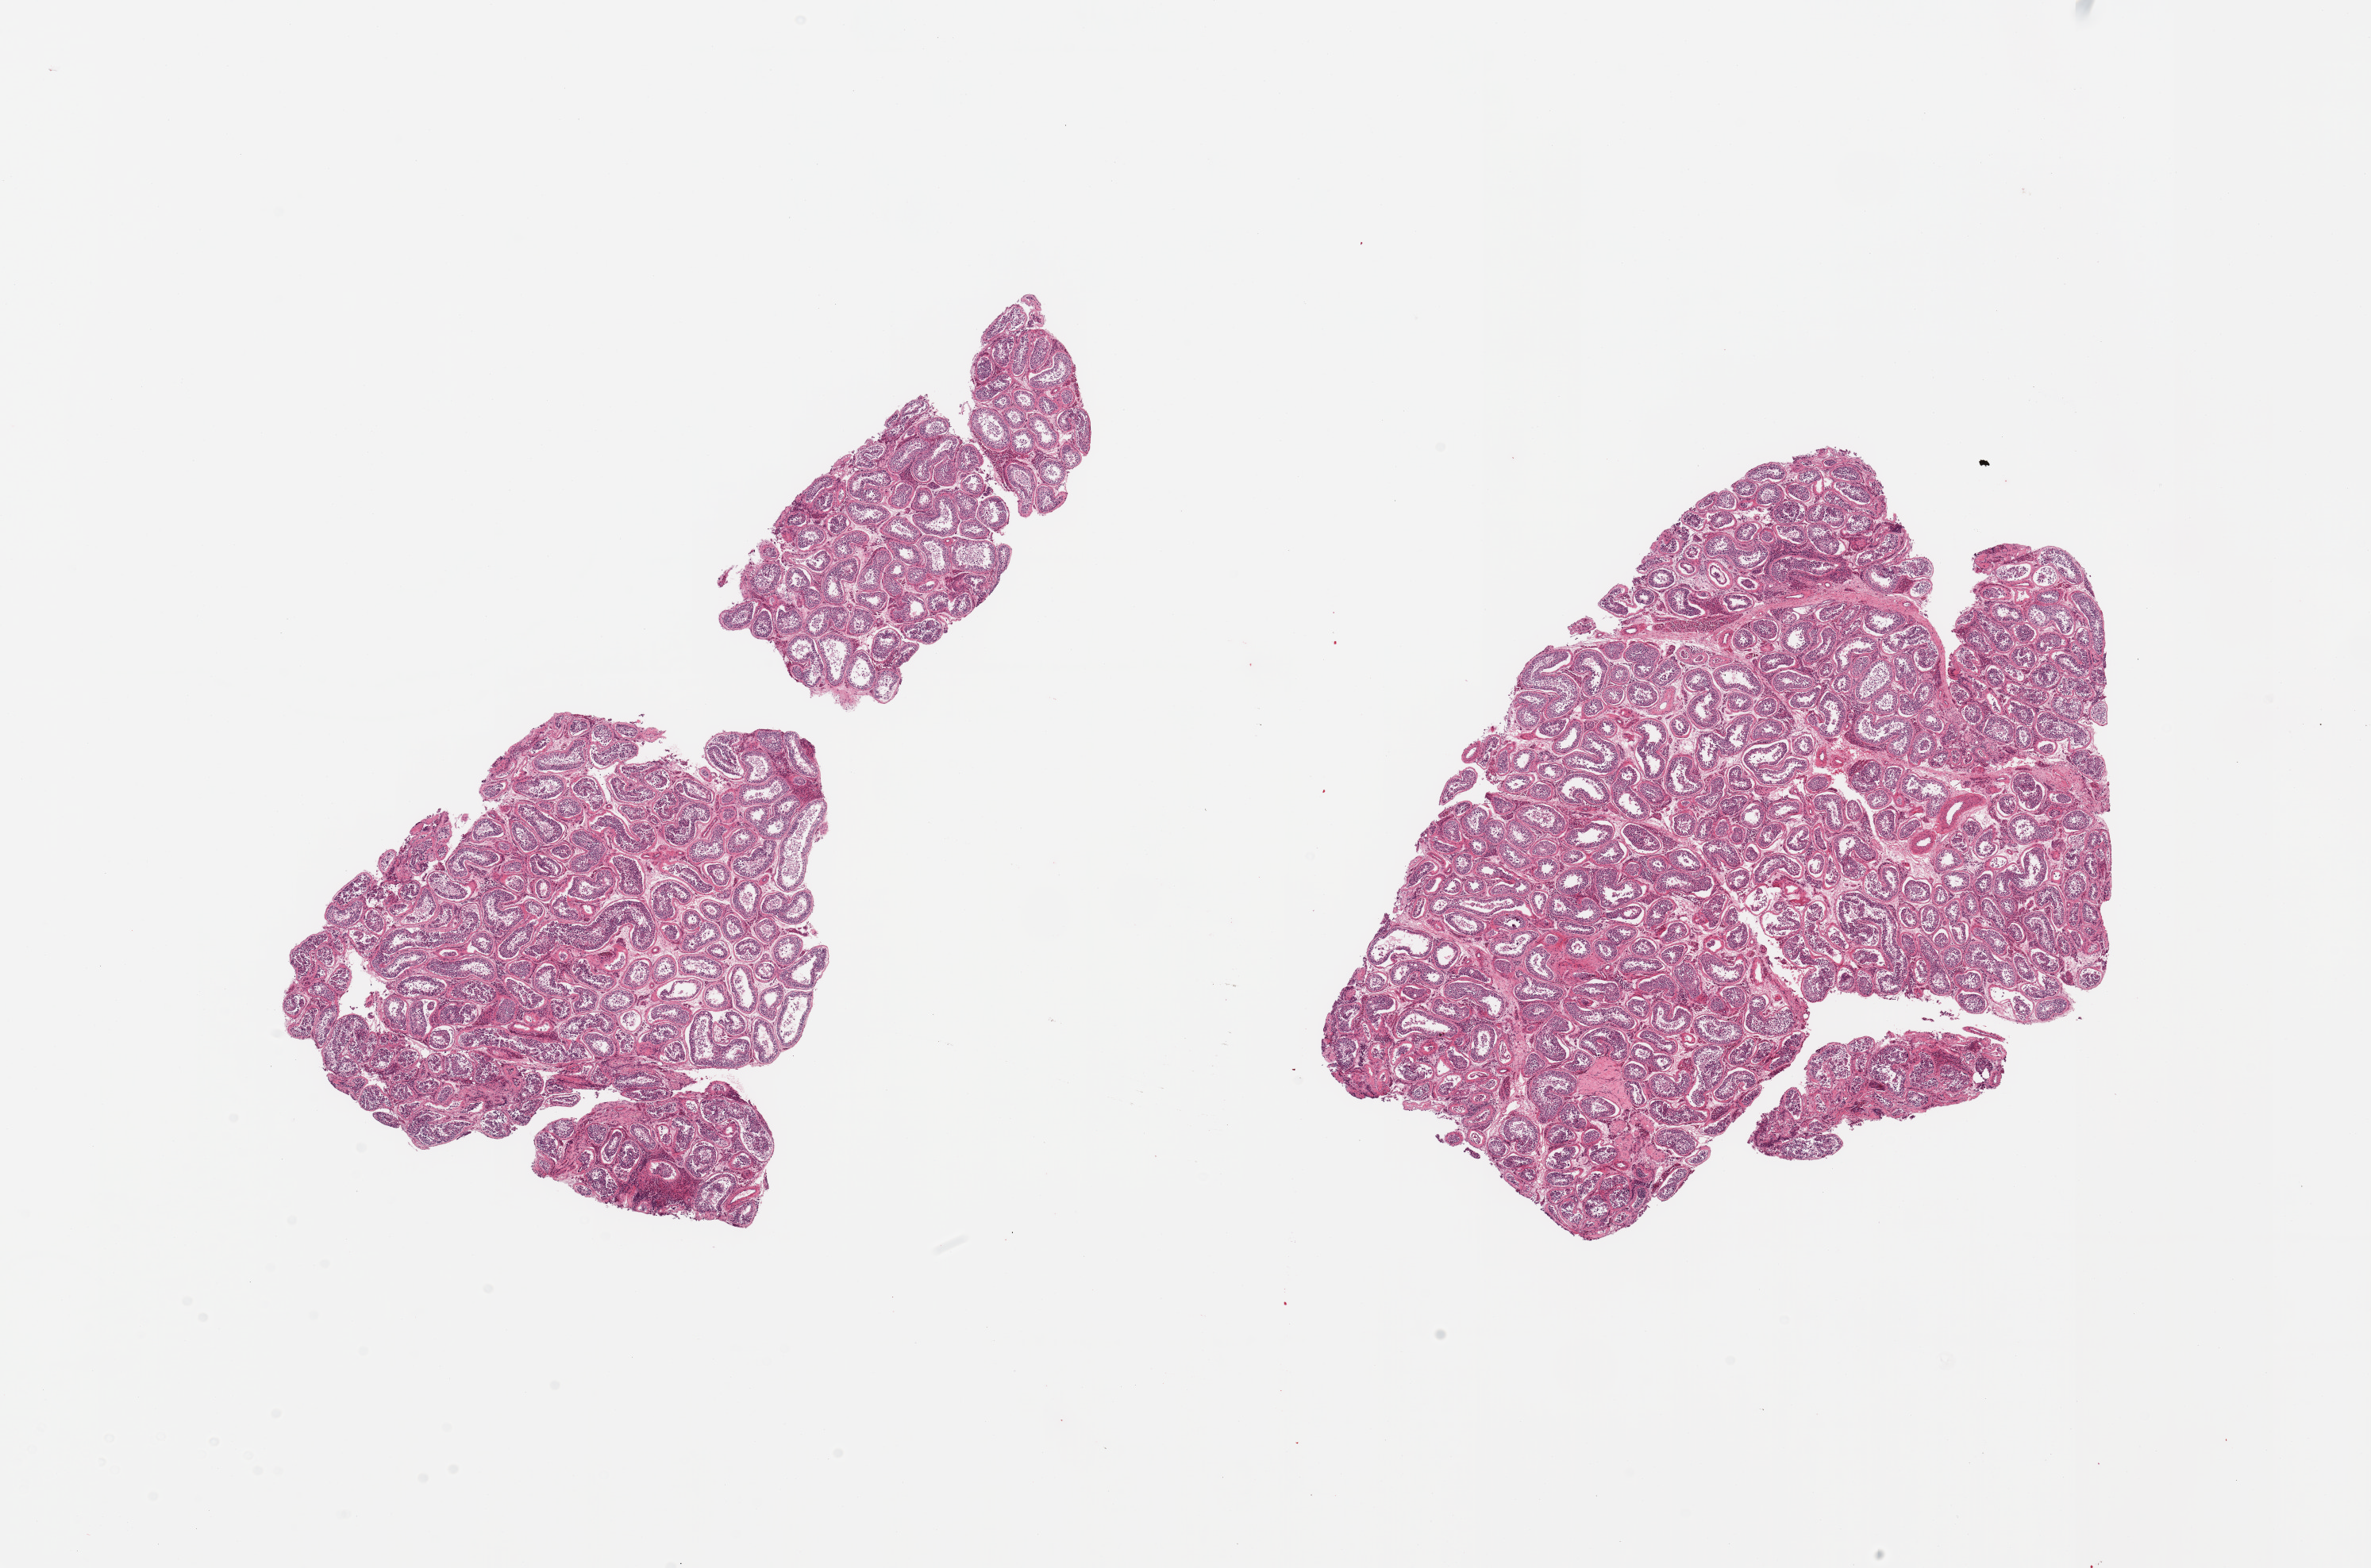
Hematoxylin and eosin (H&E) whole-slide image, low-resolution overview of the scanned area, about 23.6 x 15.6 mm (from a 20x scan), PAXgene-fixed, paraffin-embedded tissue, target tissue: testis, donor tissue sample. Donor sex: male.
* reviewer comment on this tissue sample: 2 pieces, spermatogenesis appears reduced